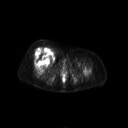
FDG PET of an extremity soft-tissue mass (from a PET/CT study), one axial slice; slice 55 of 267 in the series (ordered by position); 3.27 mm slice thickness; 128 × 128 image matrix, field of view 700 × 700 mm. Patient: female, 56 years. From the clinical record (not read from this slice): histological type: malignant solitary fibrous tumor; grade: intermediate; site of the primary tumour: right thigh.
Outlined on this slice (expert contour drawn on MRI and transferred to this co-registered scan by the dataset authors):
- gross tumour volume including surrounding oedema: box from (x=33, y=47) to (x=54, y=62) px
- gross tumour volume (mass): (x=33, y=47)–(x=53, y=62)